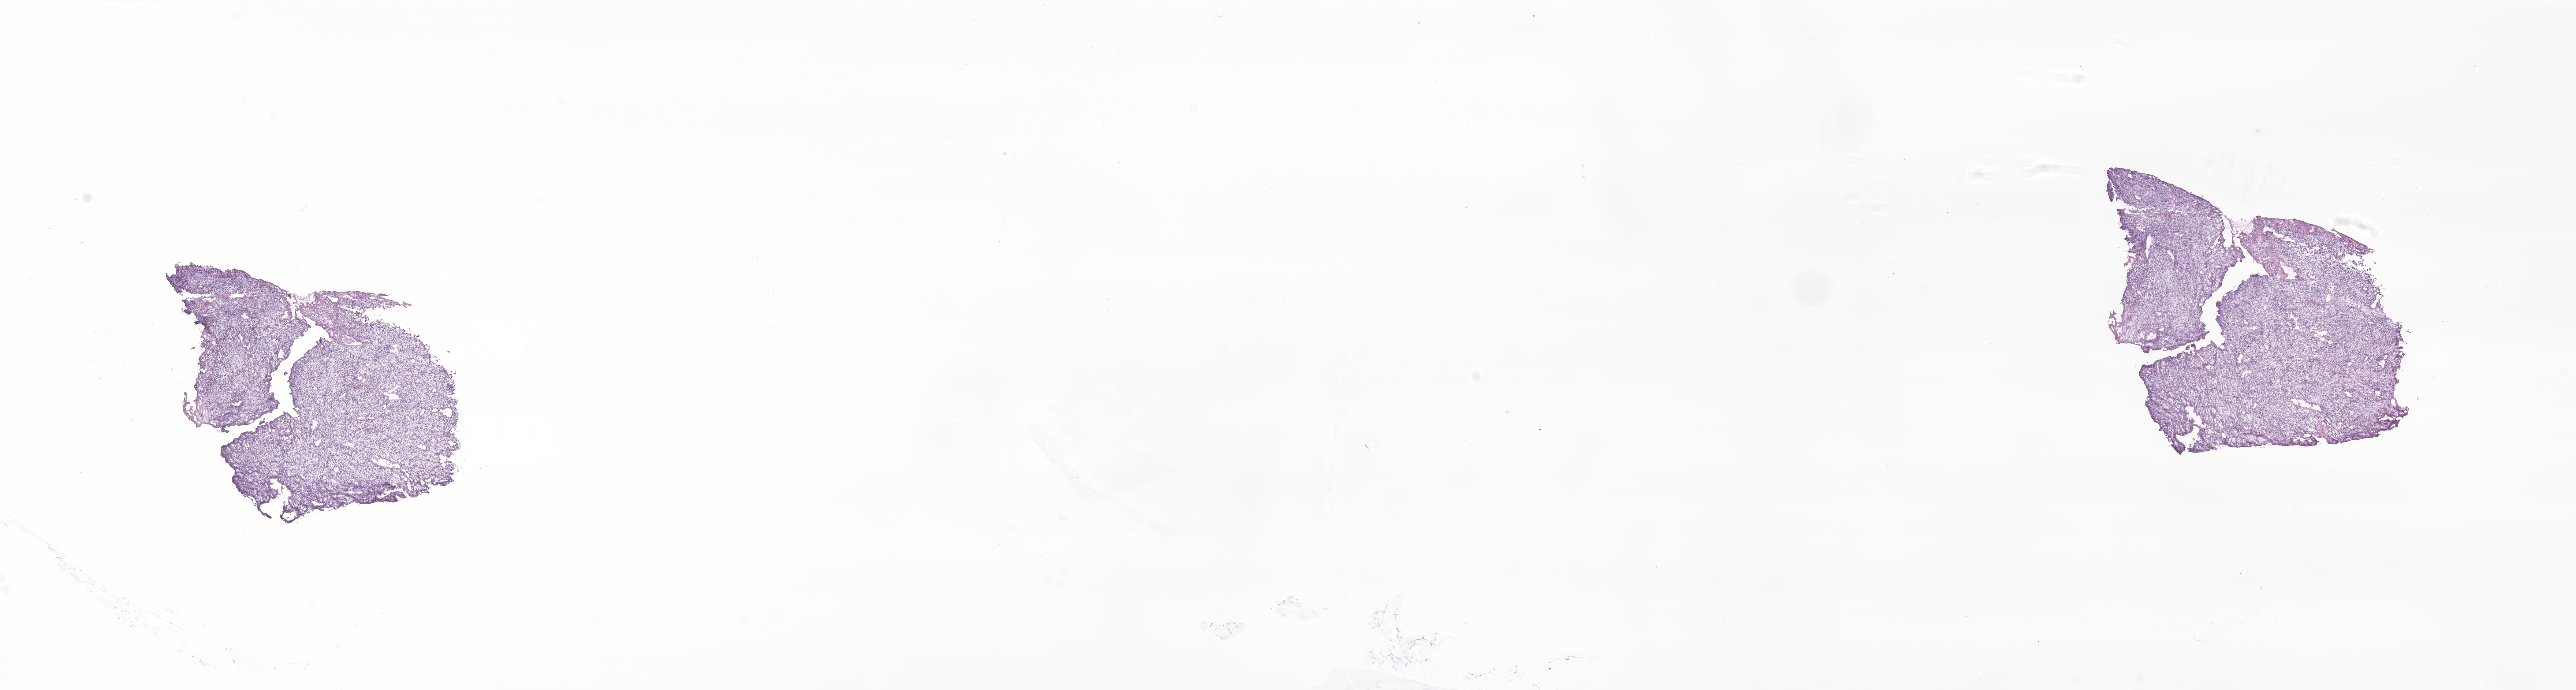
Digitized hematoxylin and eosin (H&E)-stained section of tumor tissue from the head and neck, low-resolution overview of the scanned area, about 29.7 x 7.9 mm; cryosection (OCT / tissue freezing medium). Male patient, age 132 months (11 years).
* recorded diagnosis: Embryonal rhabdomyosarcoma, NOS
* tissue or organ of origin (case record): head, face or neck